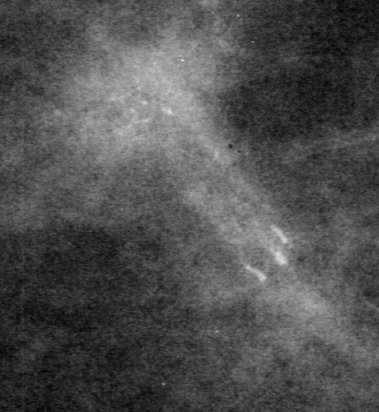
Cropped region of a digitized screen-film mammogram centred on a radiologist-marked abnormality, left breast, CC view.
- Calcifications, morphology fine linear branching, distribution clustered; BI-RADS assessment category 4; pathology (as recorded): malignant.